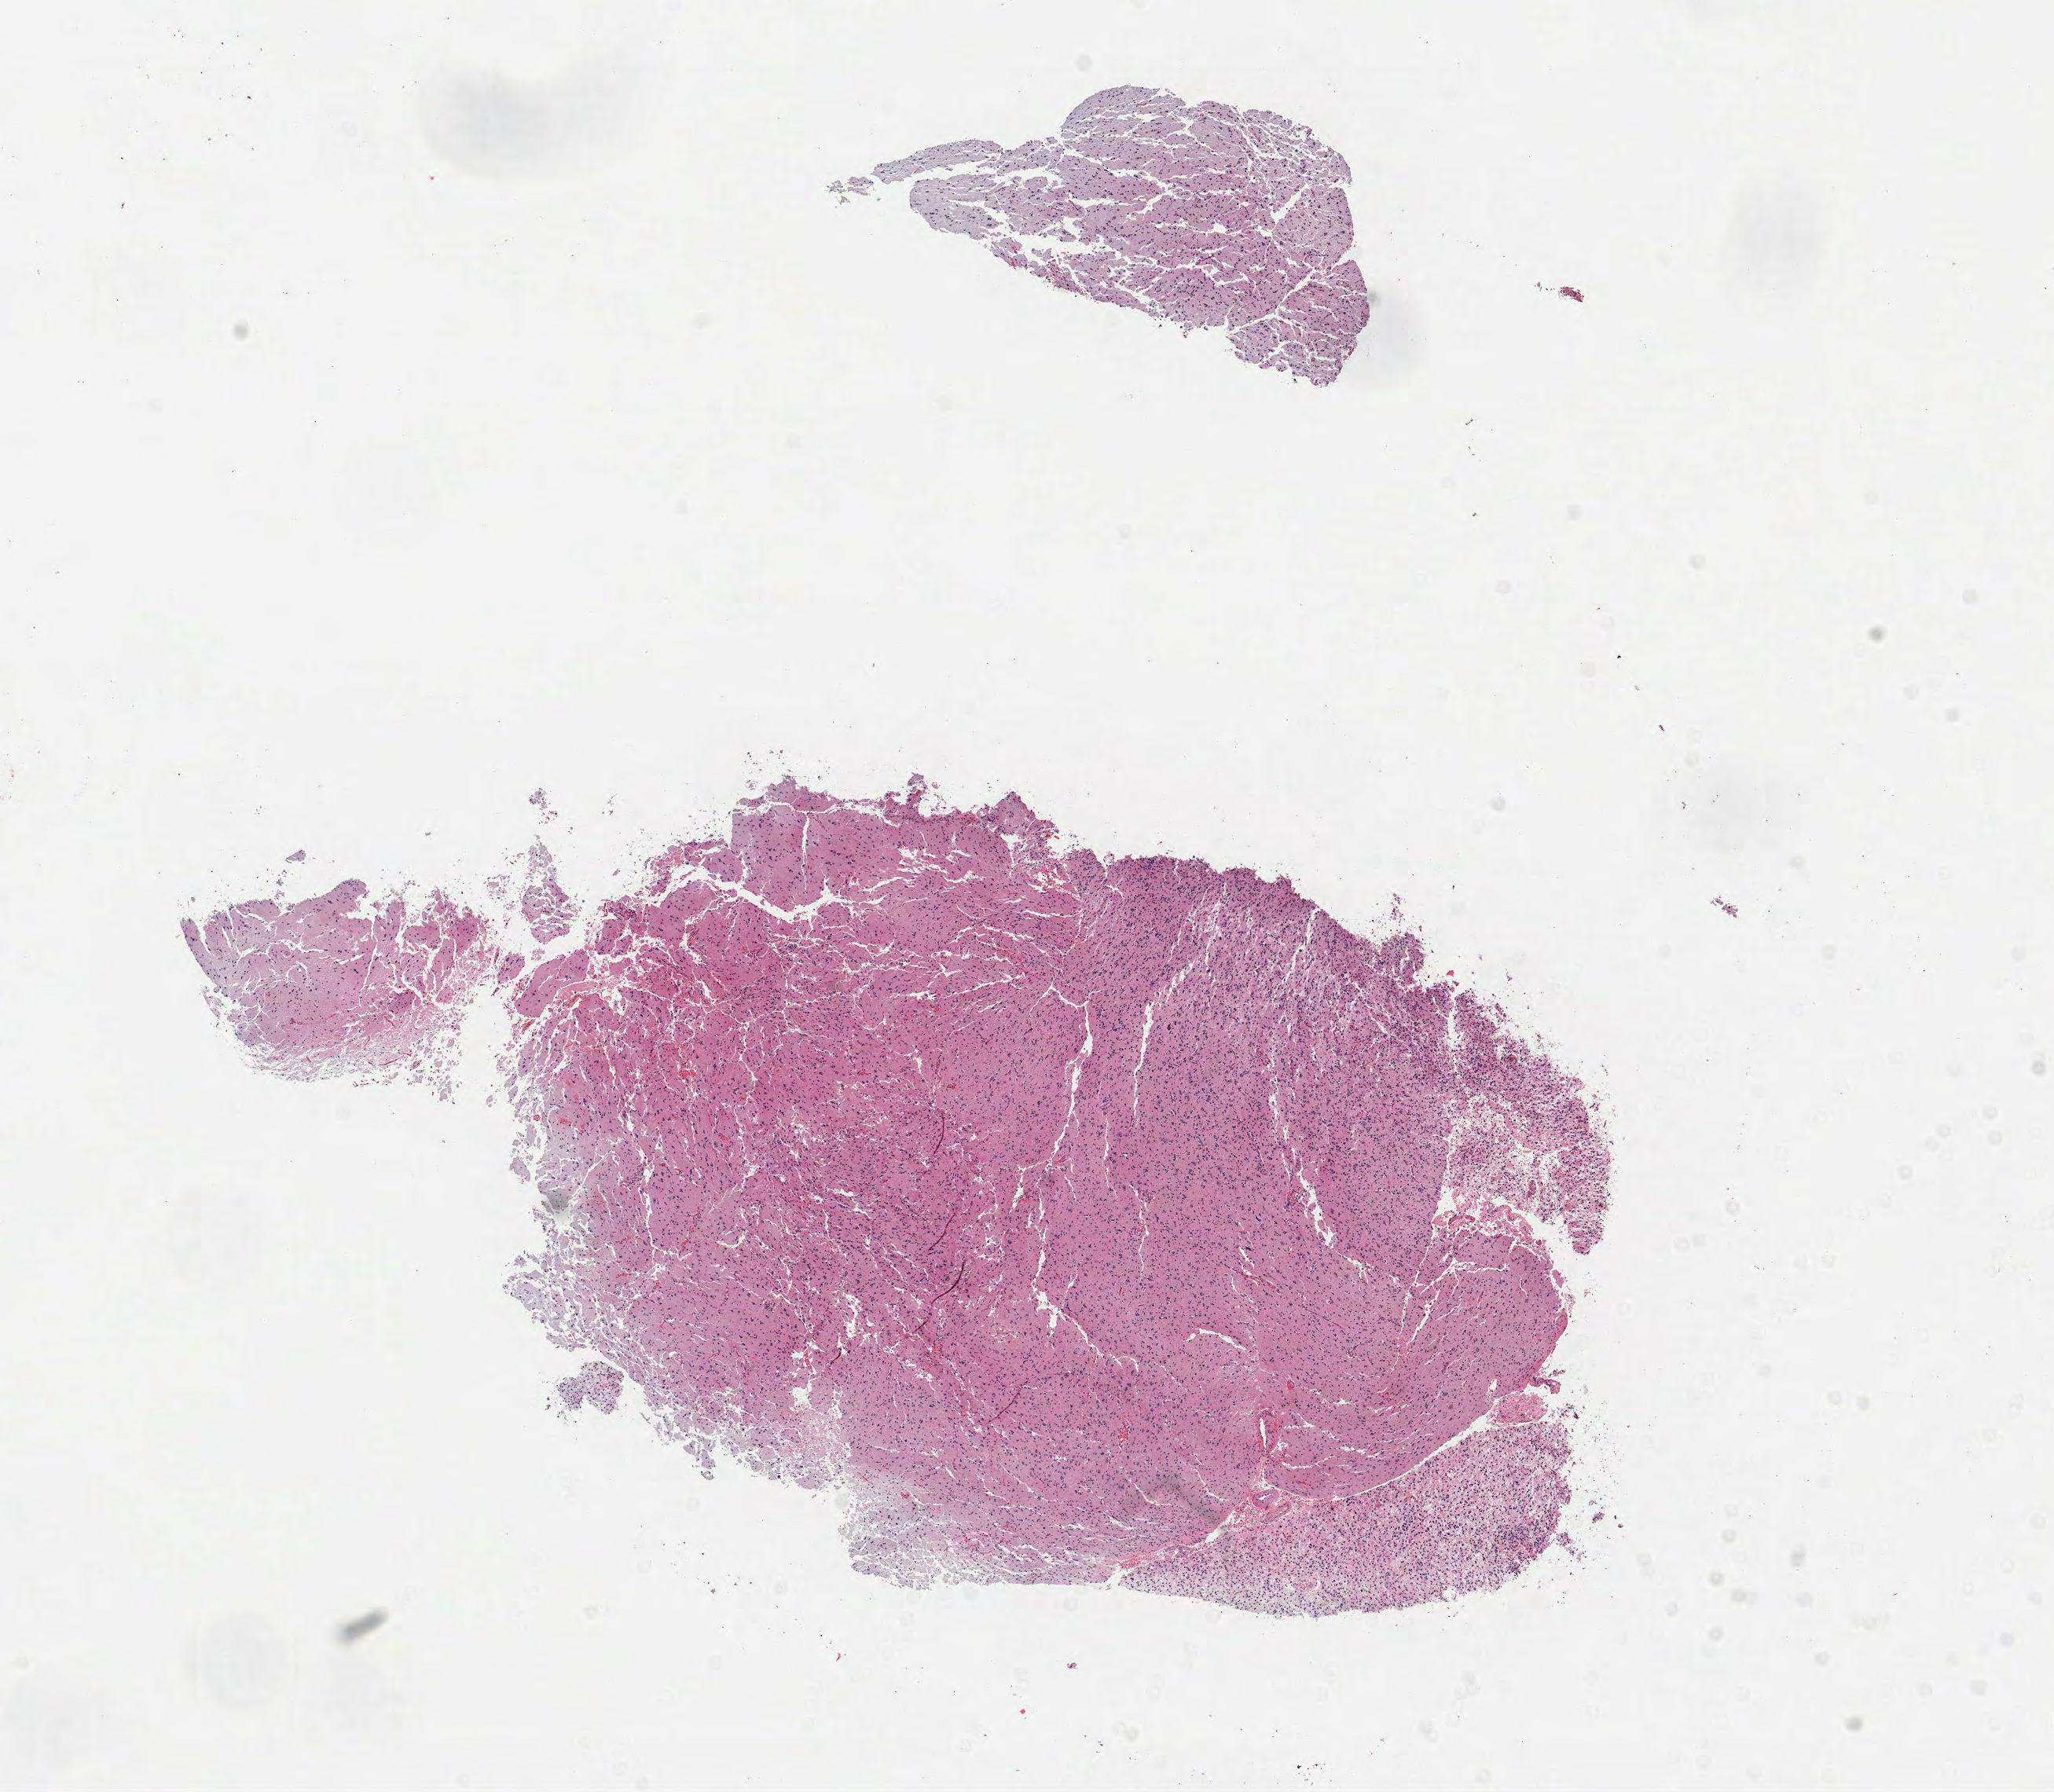
Digitized H&E tissue section (whole slide), low-resolution overview of the scanned area, about 10.5 x 9.2 mm (acquisition: 40x scan), frozen section from the top of the tissue portion, brain, primary tumour sample. Patient: male, age at initial diagnosis 23 years. Composition of this section per pathologist review: tumour cells 100%, tumour nuclei 70%.
Pathologic diagnosis: Mixed glioma (cerebrum).